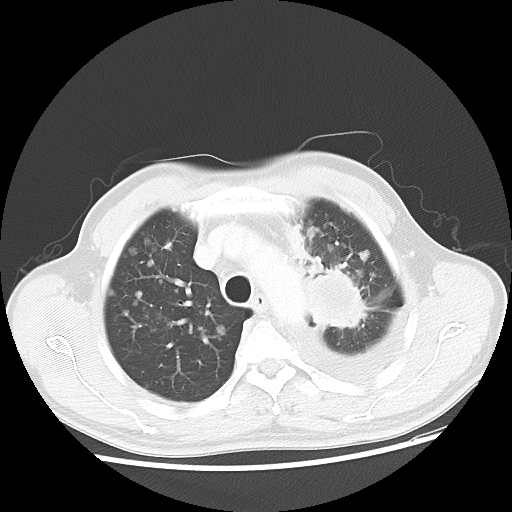
Chest CT, one axial slice. Position 36 of 47 along the scan axis. 100 kVp. Lung window (W 1500 / L -600 HU). 512 × 512 image matrix, field of view 362 × 362 mm. Male patient, age 55 years. Case-level facts recorded for this patient, not image findings: clinical TNM (as recorded): T2 N3 M1a; histopathological grade: G3.
Structures marked on this image (rectangle marked by the reading radiologist):
- lung tumour (recorded histology: squamous cell carcinoma): bounding box (x1, y1, x2, y2) in pixels: (302, 259, 380, 358)